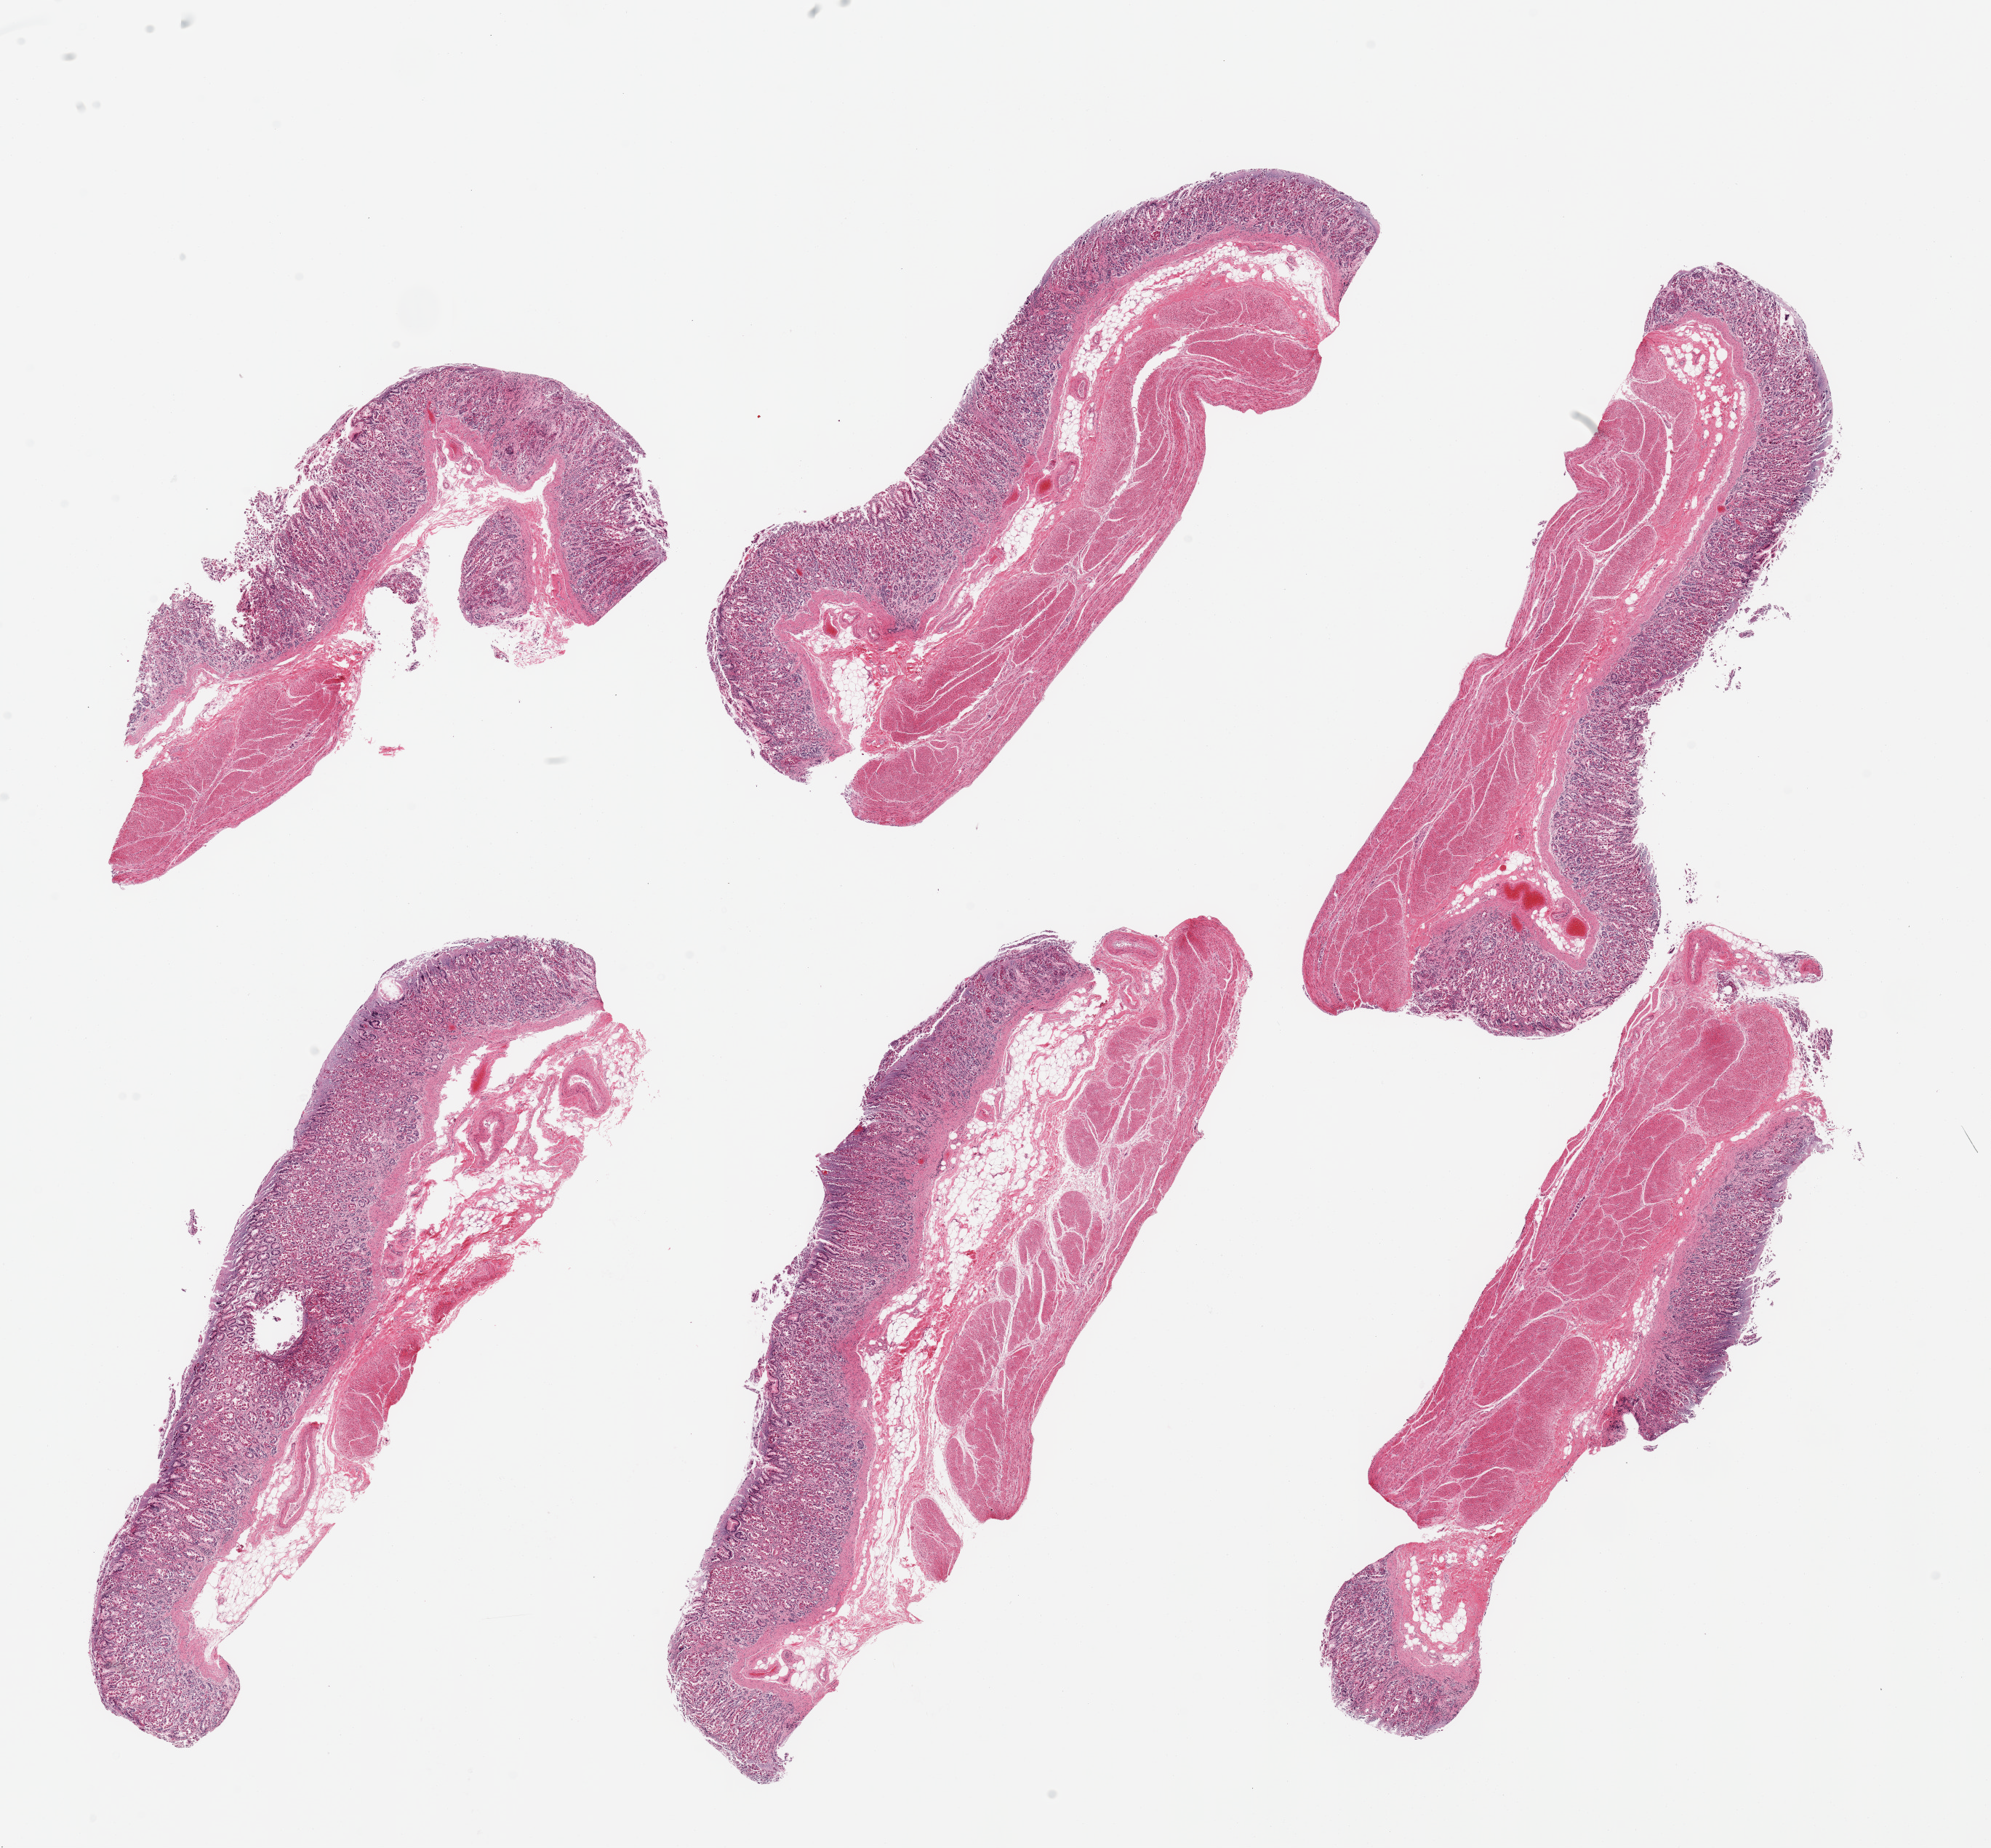
Whole-slide image, haematoxylin and eosin stain, low-resolution overview of the scanned area, about 21.7 x 20.1 mm (from a 20x scan), PAXgene-fixed paraffin-embedded (PFPE) section, sampled site (target tissue): stomach, tissue donor sample. Donor sex: female.
Pathologist's review note for this sample: 6 pieces; mucosa and muscularis, chronic gastritis.